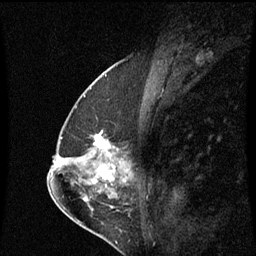
Breast MRI (dynamic contrast-enhanced), one sagittal slice. Slice 33 of 60 in the series (ordered by position). Dynamic contrast-enhanced series, image 2 of 3 at this slice position (ordered by acquisition). 1.5 T. TE 4.2 ms, TR 8.9 ms. 2 mm slice thickness. 256 × 256 image matrix, field of view 200 × 200 mm. Patient: female, 57 years. From the clinical record (not read from this slice): setting: breast cancer imaged before/during neoadjuvant chemotherapy; receptor status: HR-positive, HER2-negative.
Outlined on this slice (semi-automatic segmentation, software-assisted and operator-edited):
- analysis volume of interest (the breast-tissue region the enhancement analysis was run in; not a lesion): bounding box <83,132,117,159> (left, top, right, bottom; pixels)
- tumour enhancement mask (voxels above the 70 % enhancement threshold inside the analysis volume of interest): <94,134,111,157>